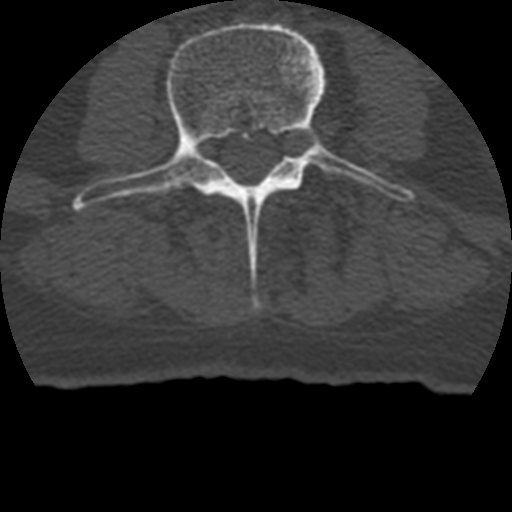
CT including the spine, one axial slice. 120 kVp. Bone window (W 1800 / L 400 HU). 1.25 mm slice thickness. 512 × 512 image matrix. Patient age 69 years. Case-level facts recorded for this patient, not image findings: primary cancer: prostate.
Outlined on this slice (semi-automatic segmentation, software-assisted and operator-edited):
- L3 vertebra: bounding box <77,22,412,309> (left, top, right, bottom; pixels)